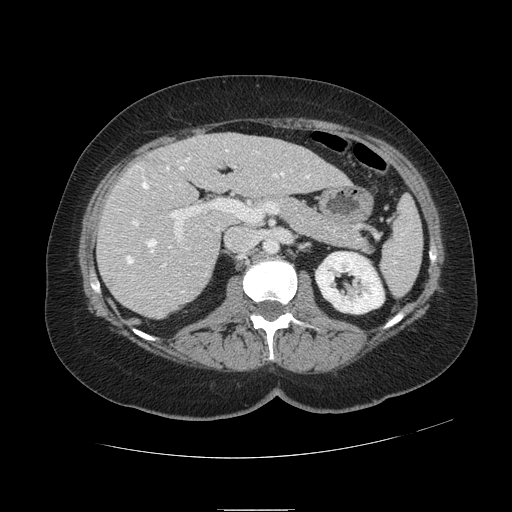
Contrast-enhanced abdominal CT, one axial slice; slice 52 of 121 in the series (ordered by position); intravenous contrast given; soft-tissue window (W 400 / L 40 HU); 2.5 mm slice thickness; 512 × 512 image matrix. Female patient, age 52 years. From the clinical record (not read from this slice): diagnosis: colorectal cancer liver metastases, imaged before liver resection; multiple liver metastases: yes; largest metastasis: 6.3 cm; disease in both lobes: no.
Outlined on this slice (expert manual segmentation):
- hepatic veins: bounding box [x1, y1, x2, y2] px = [127, 150, 309, 293]
- liver: [99, 133, 347, 317]
- planned liver remnant (the part of the liver to remain after resection): [171, 134, 347, 197]
- portal vein (with intrahepatic branches): [132, 166, 292, 267]